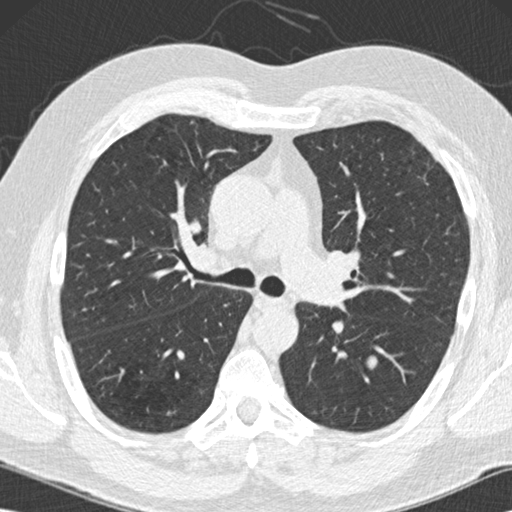
Low-dose screening chest CT, one axial slice; slice 91 of 152 in the series (ordered by position); reconstruction kernel B30f; lung window (W 1500 / L -600 HU); 2 mm slice thickness; 512 × 512 image matrix, field of view 350 × 350 mm.
Annotated regions visible in this slice (manually delineated by an expert):
- lesion 2 (nodule, lower lobe of left lung): bounding box (x1, y1, x2, y2) in pixels: (367, 356, 377, 369)